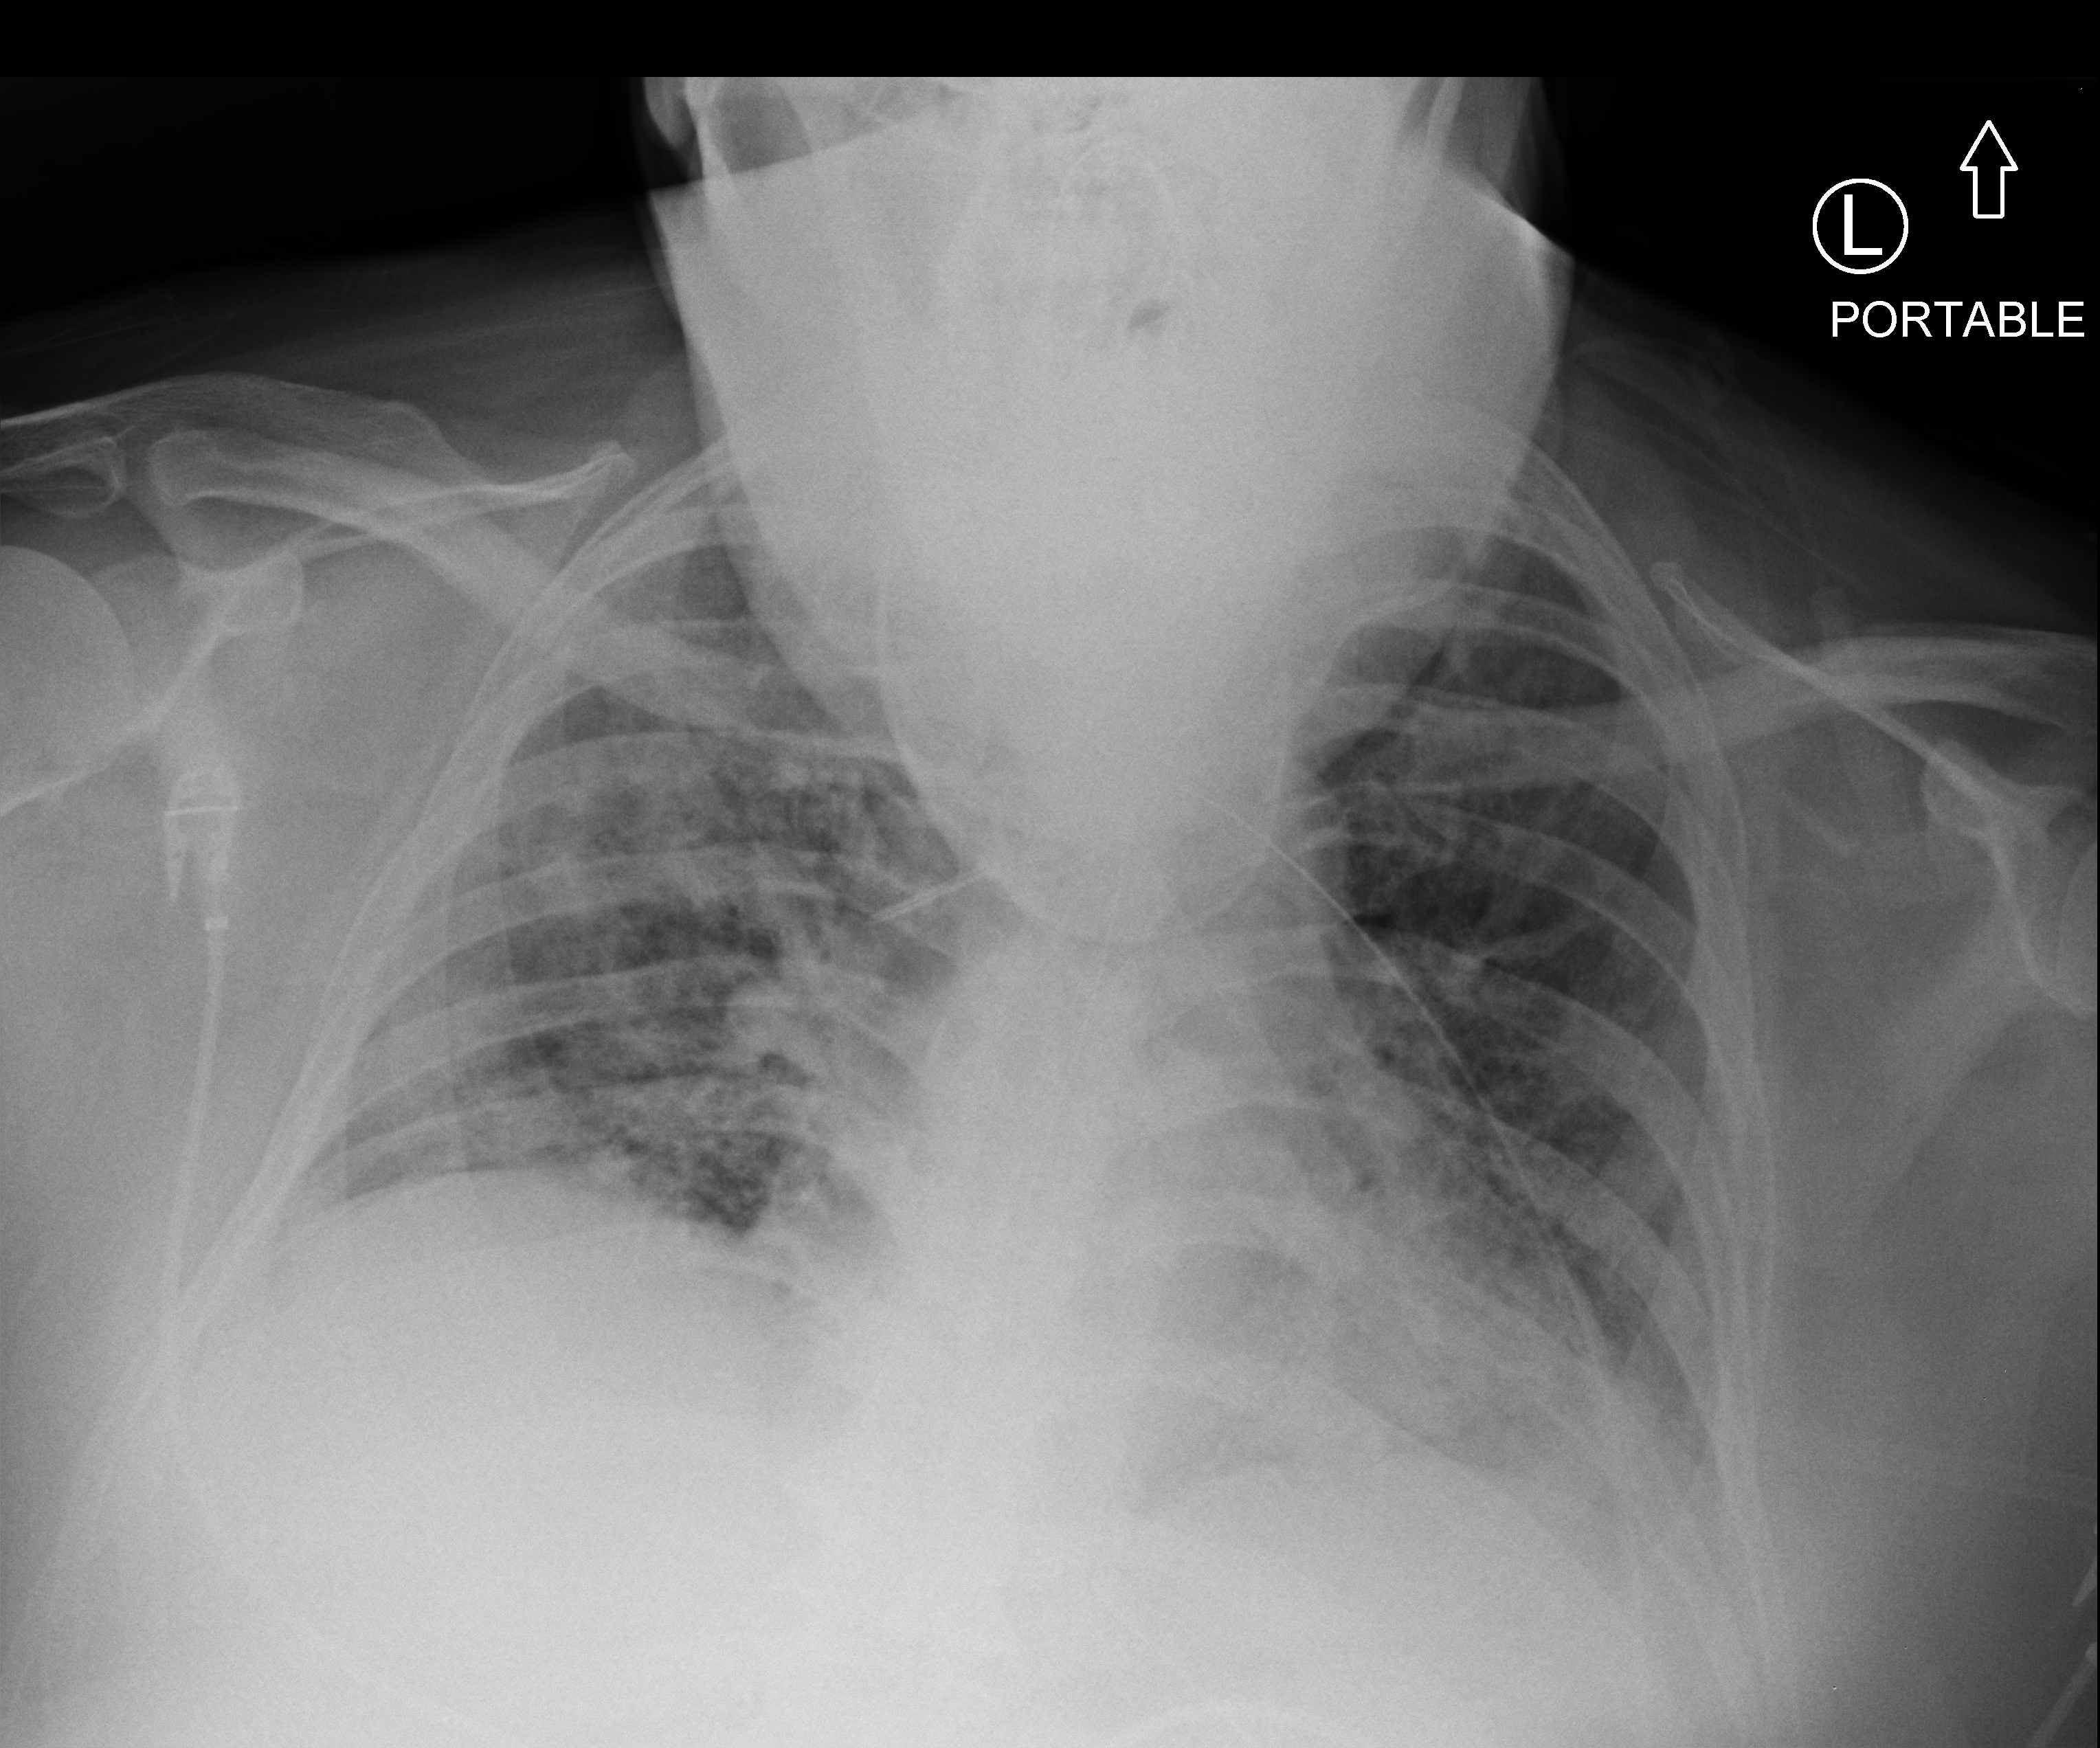
Portable chest radiograph; anteroposterior (AP) projection. Male patient hospitalised with COVID-19, age 18–59 years.
From the hospital-stay record, not from the radiograph (when in the stay this image was taken is not recorded): admitted to intensive care during this hospital stay: yes.